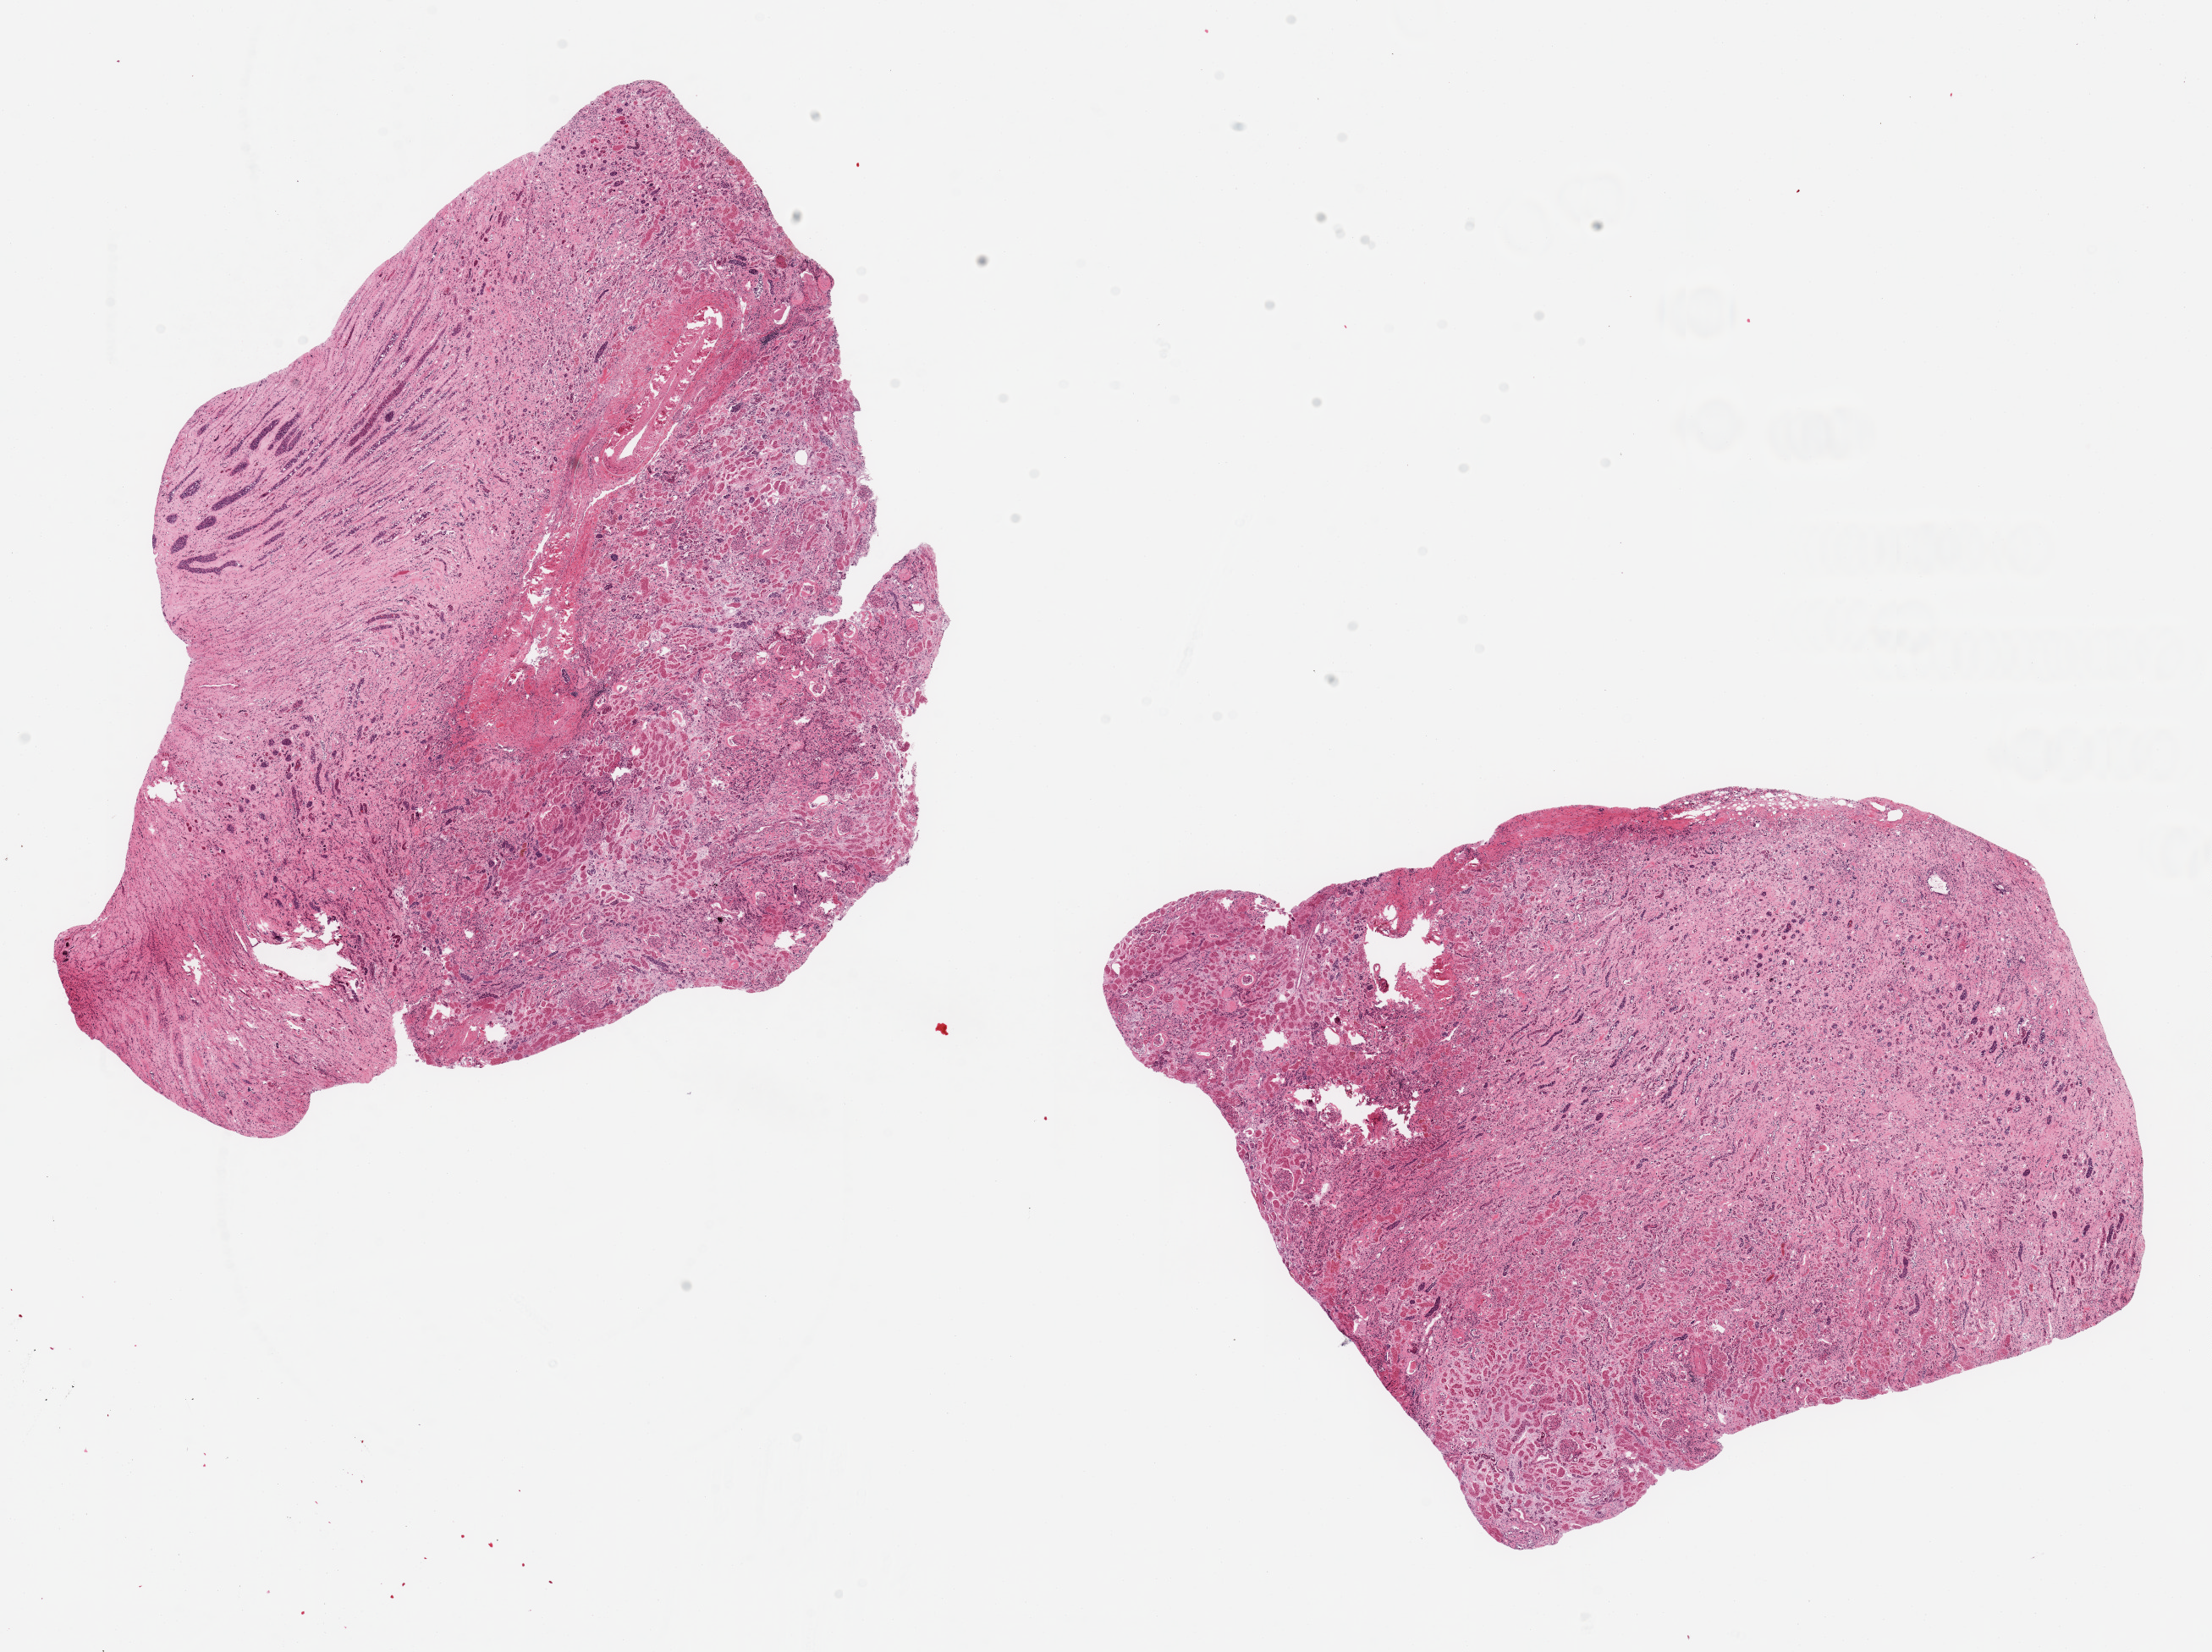
Hematoxylin and eosin (H&E) whole-slide image, brightfield, shown as a low-resolution overview of the whole scanned area (about 20.7 x 15.4 mm, acquisition: 20x scan). PAXgene-fixed, paraffin-embedded tissue. Target tissue: renal medulla. Tissue donor sample. Male donor.
Pathologist's review note for this sample: 2 ~10x6.3mm pieces. Markedly autolyzed.